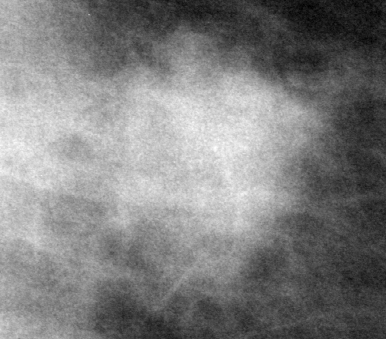
Cropped region of a digitized screen-film mammogram centred on a radiologist-marked abnormality, left breast, MLO view.
Mass, shape lobulated, margins microlobulated; BI-RADS assessment category 5; pathology (as recorded): malignant.